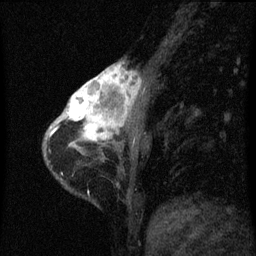
Breast MRI (dynamic contrast-enhanced), one sagittal slice; slice 14 of 60 in the series (ordered by position); dynamic contrast-enhanced series, image 2 of 3 at this slice position (ordered by acquisition); 1.5 T; TE 4.2 ms, TR 8 ms; 2 mm slice thickness; 256 × 256 image matrix, field of view 180 × 180 mm. Patient: female, 38 years.
Structures marked on this image (semi-automatically segmented with operator editing):
- analysis volume of interest (the breast-tissue region the enhancement analysis was run in; not a lesion): bounding box (x1, y1, x2, y2) in pixels: (61, 66, 144, 147)
- tumour enhancement mask (voxels above the 70 % enhancement threshold inside the analysis volume of interest): (66, 66, 139, 147)